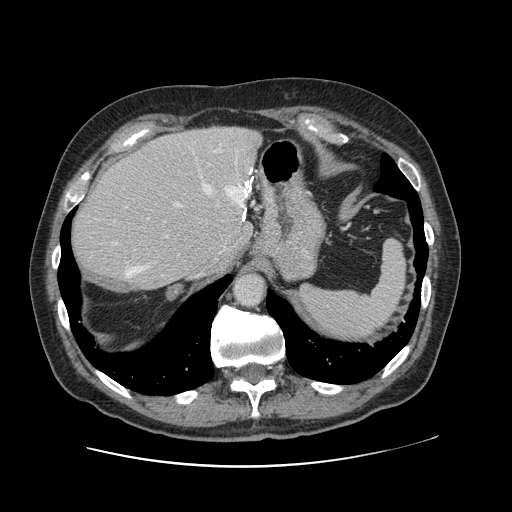
Contrast-enhanced abdominal CT, one axial slice. Position 90 of 138 along the scan axis. 120 kVp. Soft-tissue window (W 400 / L 40 HU). 512 × 512 image matrix. Male patient, age 71 years. Case-level facts recorded for this patient, not image findings: diagnosis: colorectal cancer liver metastases, imaged before liver resection; multiple liver metastases: no; largest metastasis: 3.3 cm; disease in both lobes: no.
Structures marked on this image (outlined manually by an expert reader):
- hepatic veins: bounding box (x1, y1, x2, y2) in pixels: (126, 182, 248, 278)
- liver: (72, 127, 261, 290)
- planned liver remnant (the part of the liver to remain after resection): (71, 154, 241, 290)
- portal vein (with intrahepatic branches): (111, 202, 183, 245)